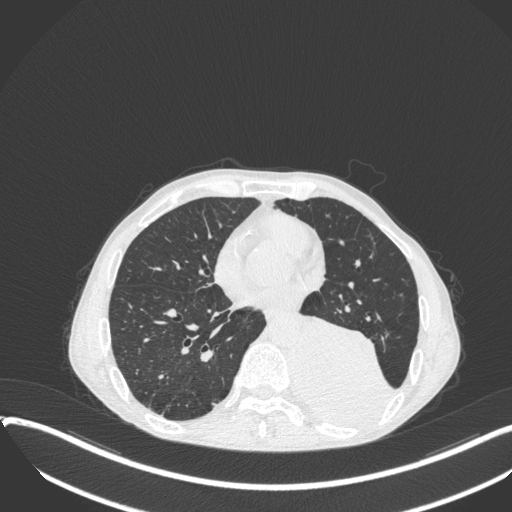
Chest CT, one axial slice. Position 148 of 400 along the scan axis. Reconstruction kernel B31f. 120 kVp. Lung window (W 1500 / L -600 HU). 1 mm slice thickness. 512 × 512 image matrix, field of view 400 × 400 mm. Patient: male, 57 years. Case-level facts recorded for this patient, not image findings: clinical TNM (as recorded): T4 N0 M0.
Annotated regions visible in this slice (bounding box drawn by a radiologist):
- lung tumour (recorded histology: squamous cell carcinoma): bounding box <290,304,391,436> (left, top, right, bottom; pixels)